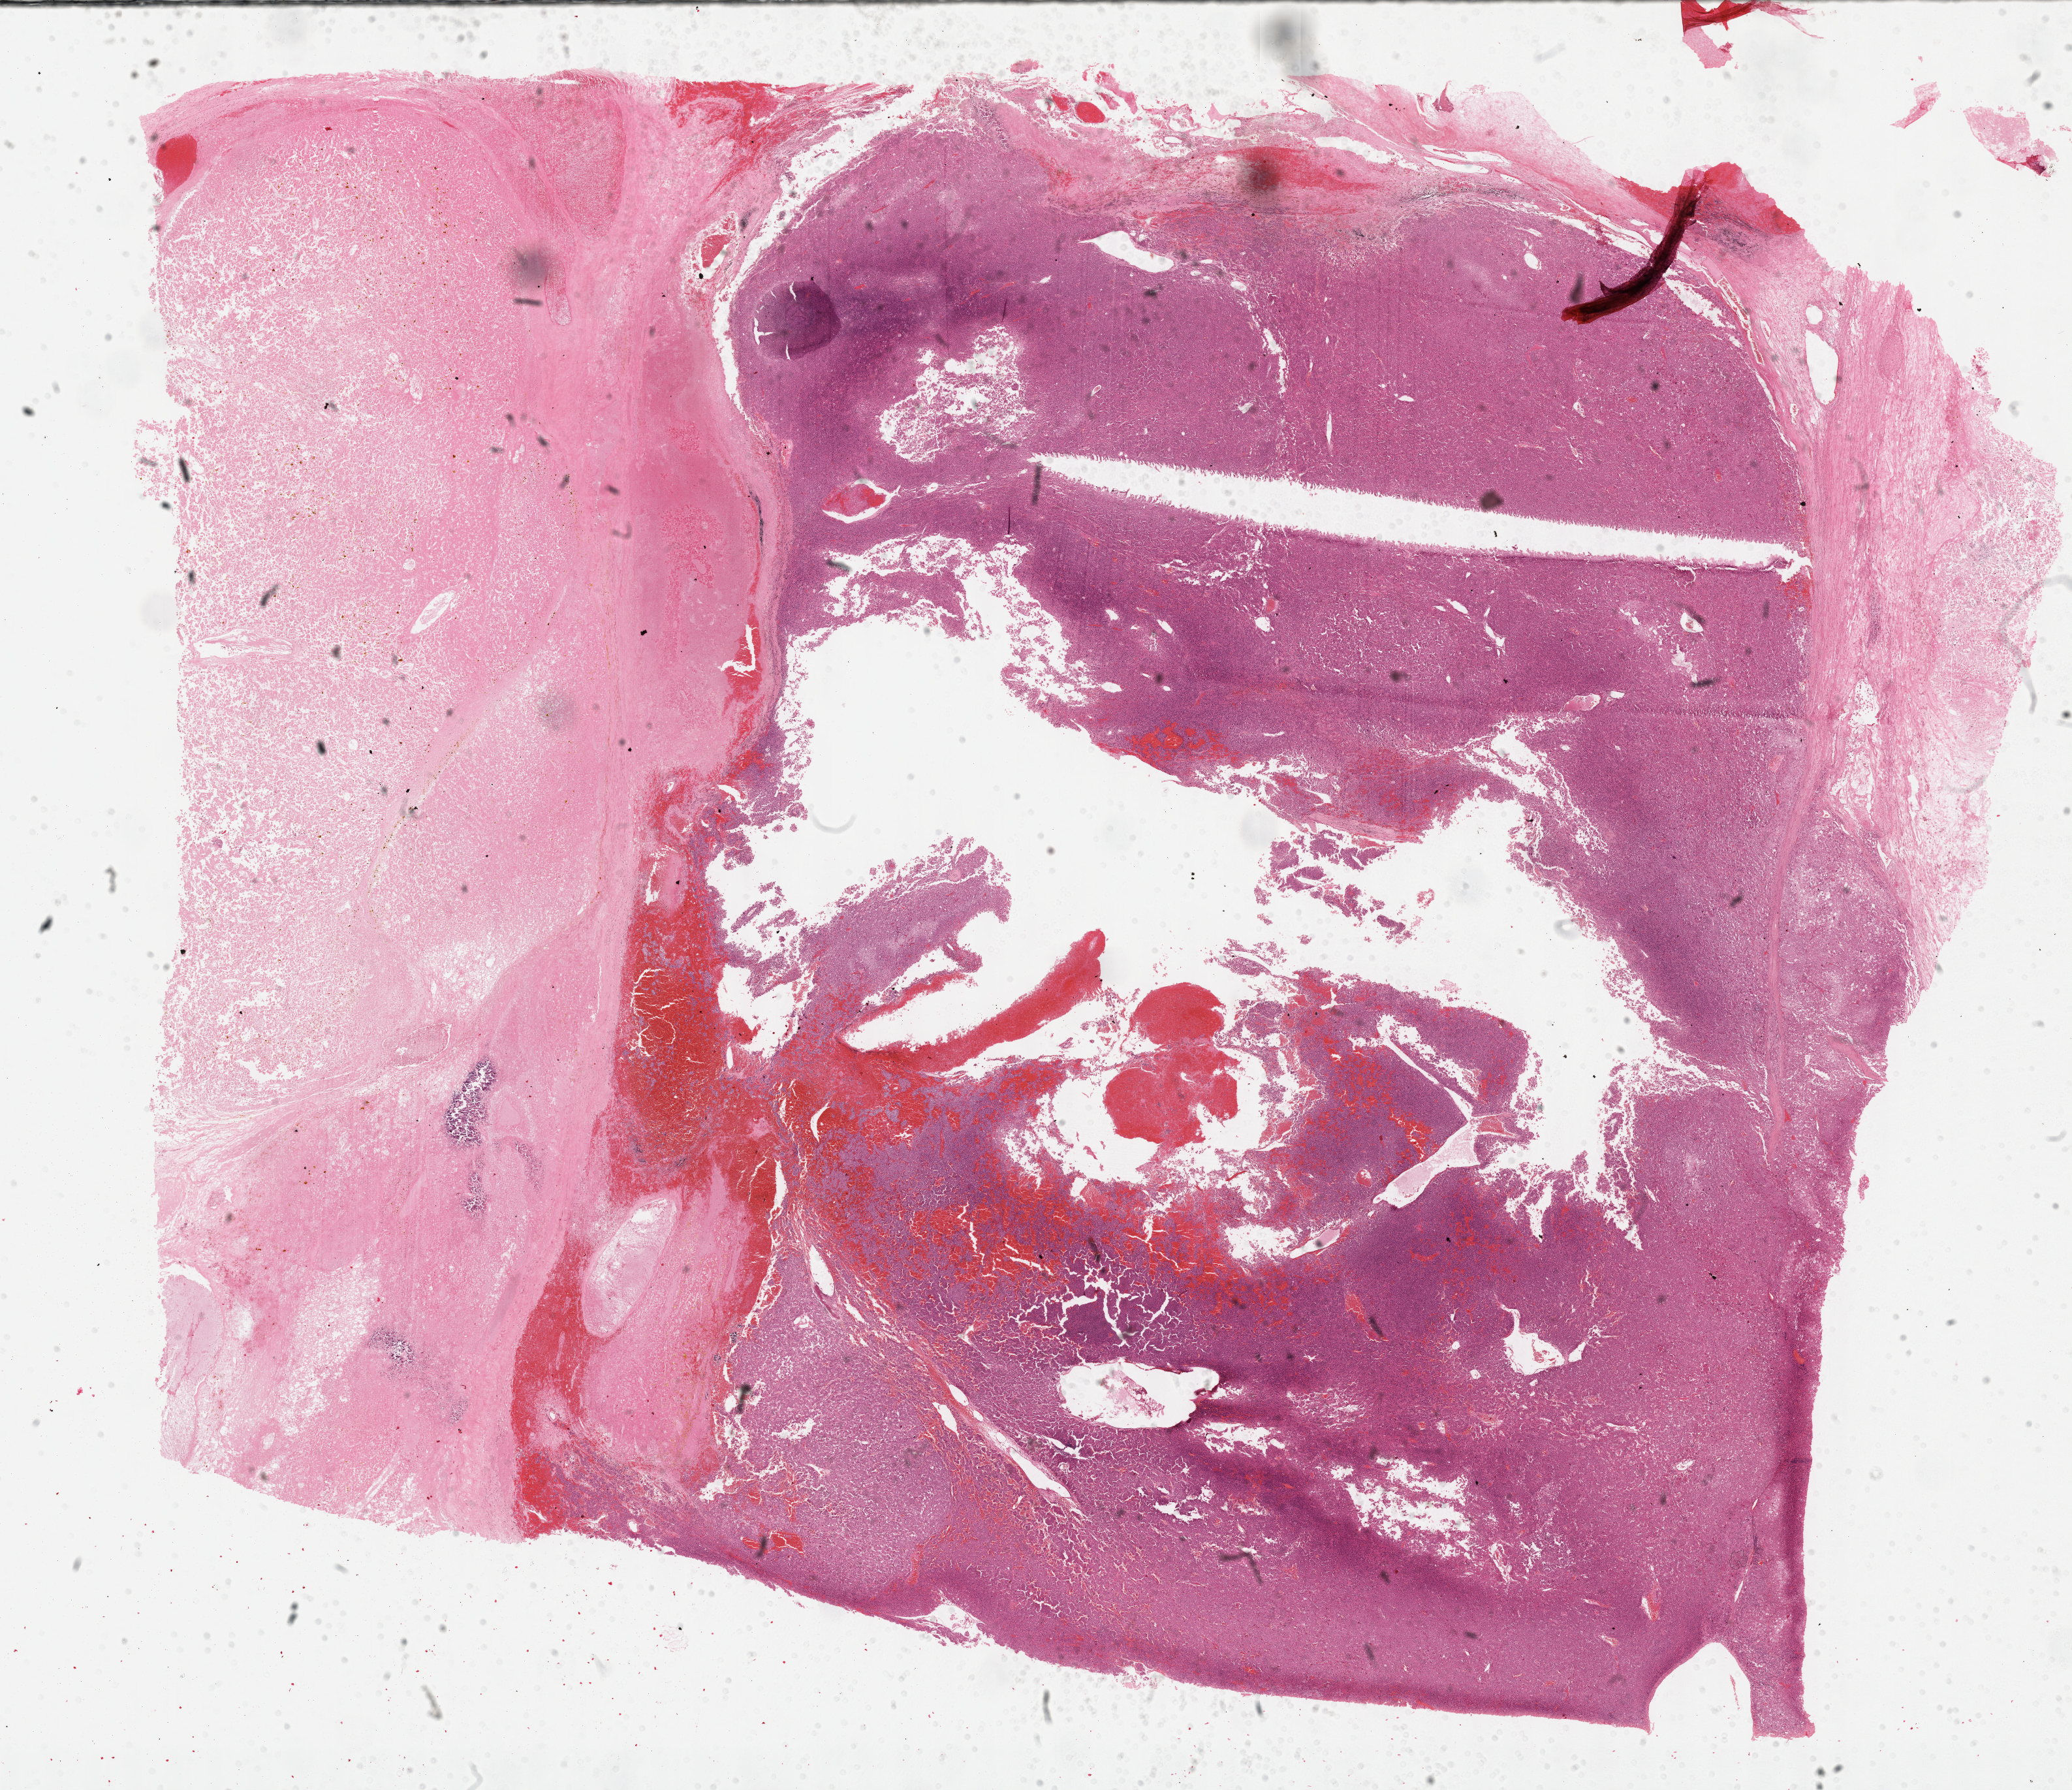
Whole-slide histology image, H&E-stained, low-resolution overview of the scanned area, about 25.7 x 22.2 mm (slide scanned at 40x). Formalin-fixed paraffin-embedded (FFPE) diagnostic section. Sample: primary tumour, adrenal cortex. Male patient; age at initial diagnosis 49 years.
• histologic diagnosis: Adrenal cortical carcinoma (cortex of adrenal gland)